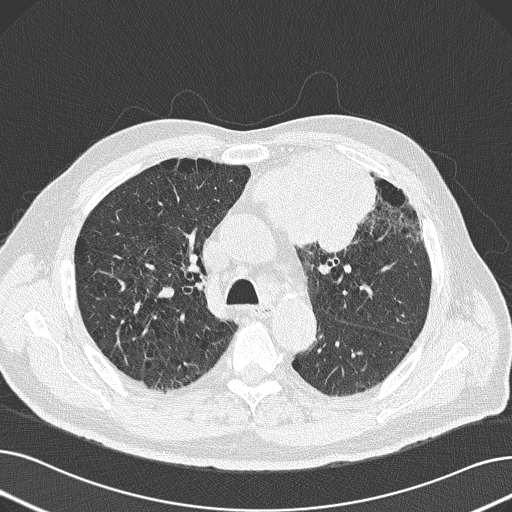
Chest CT (low-dose screening protocol), one axial image, baseline screening round, lung window (W 1500 / L -600 HU), 512 × 512 image matrix, field of view 370 × 370 mm. Male, age 69 years at enrolment. Former smoker at enrolment.
• Lesion marked by an expert reader, bounding box <229,143,381,253> (left, top, right, bottom; pixels).
• The exam's reader record, not a measurement of the box and not confirmed to be the same lesion: non-calcified nodule or mass ≥4 mm, left upper lobe, 6 × 10 mm, spiculated (stellate) margins, soft tissue attenuation.
• Official screen result: positive, change unspecified: nodule(s) >= 4 mm or enlarging nodule(s), mass(es), or other non-specific abnormalities suspicious for lung cancer.
• Participant outcome: lung cancer diagnosed 20 days after this screen — non-small cell carcinoma, left upper lobe, poorly differentiated (G3), stage IB (AJCC 6th edition), 100 mm at pathology.